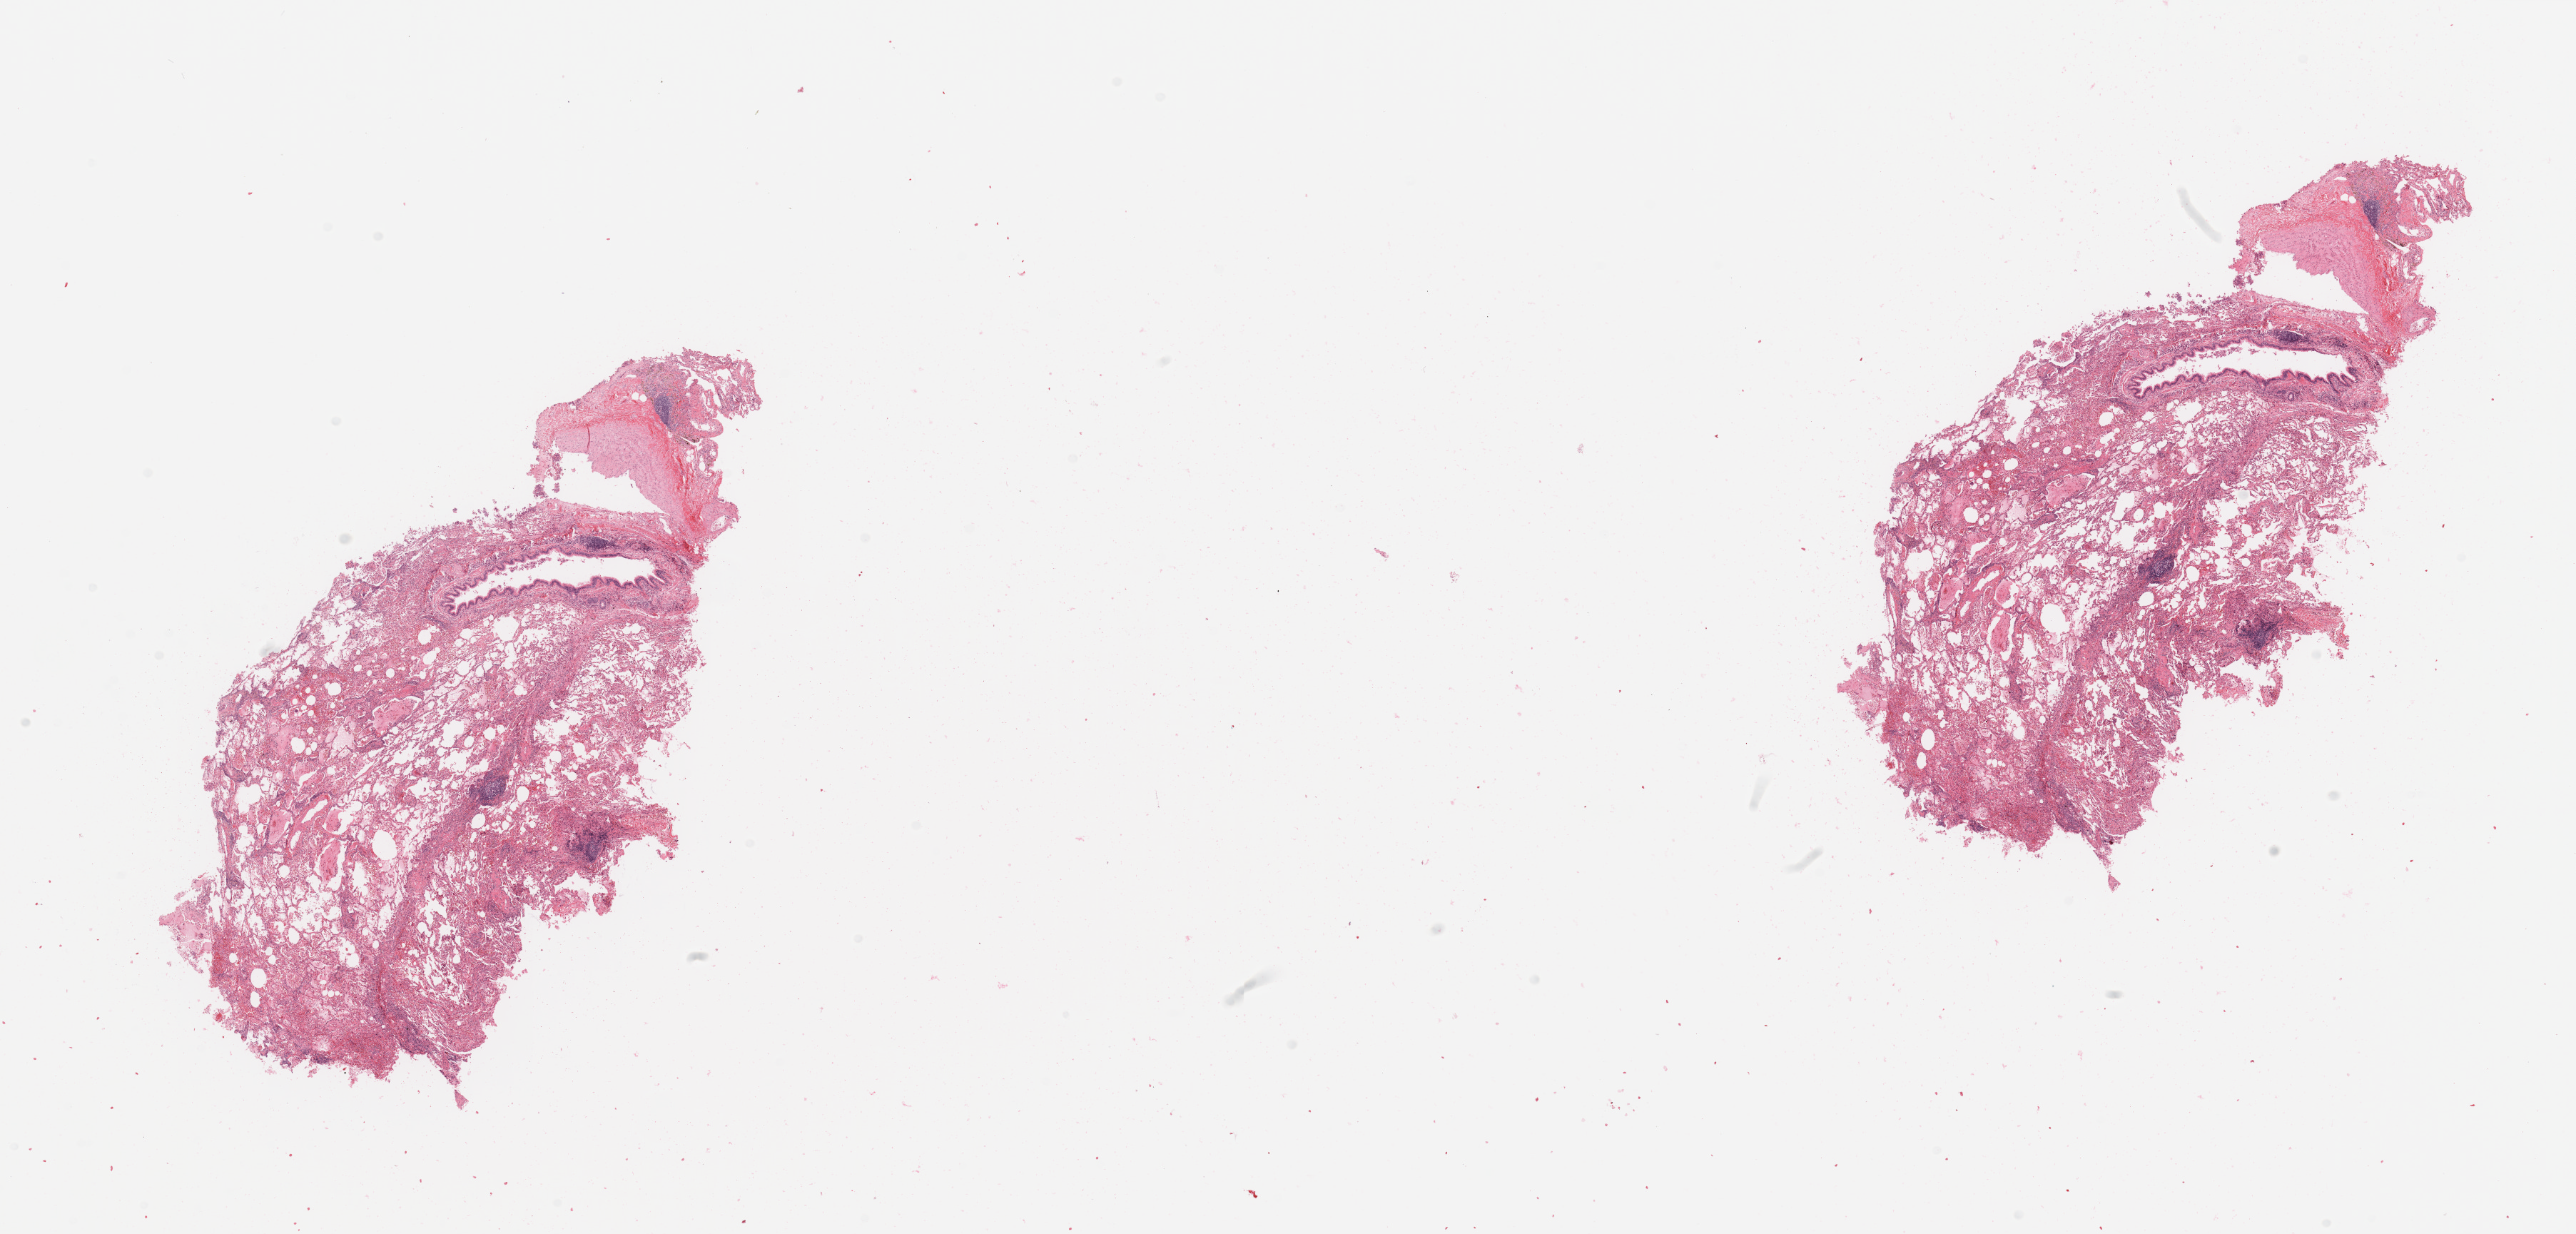
Whole-slide histology image, H&E-stained, low-resolution overview of the scanned area, about 28.5 x 13.7 mm (from a 20x scan). Normal (non-tumour) tissue sample, lung. Female, 47 y/o.
This section: normal (non-tumour) tissue from the same patient. Patient diagnosis: Adenocarcinoma, NOS.